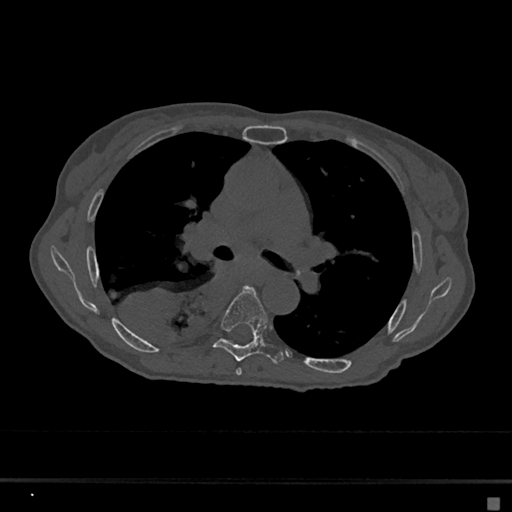
CT including the spine, one axial slice. Position 420 of 797 along the scan axis. 120 kVp. Bone window (W 1800 / L 400 HU). 0.5 mm slice thickness. 512 × 512 image matrix, field of view 360 × 360 mm. Female patient, age 68 years. From the clinical record (not read from this slice): primary cancer: renal.
Outlined on this slice (semi-automatic segmentation, software-assisted and operator-edited):
- T5 vertebra: bounding box [x1, y1, x2, y2] px = [236, 368, 242, 376]
- T6 vertebra: [213, 286, 284, 363]